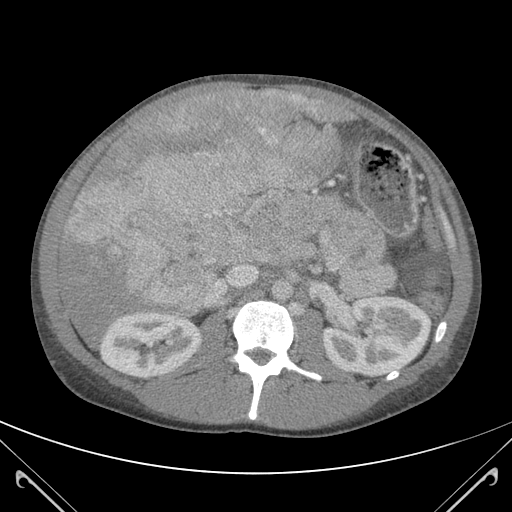
Contrast-enhanced abdominal CT (liver protocol), one axial slice; slice 61 of 118 in the series (ordered by position); 120 kVp; soft-tissue window (W 400 / L 40 HU); 512 × 512 image matrix, field of view 380 × 380 mm. From the clinical record (not read from this slice): diagnosis: hepatocellular carcinoma (patient treated with transarterial chemoembolisation; whether this scan precedes or follows treatment is not stated here); TNM stage (as recorded): Stage-IIIB; Child-Pugh class: A; tumour nodularity: uninodular.
Structures marked on this image (semi-automatic segmentation, software-assisted and operator-edited):
- abdominal aorta: bounding box <272,279,291,300> (left, top, right, bottom; pixels)
- liver parenchyma outside the tumour (the mass and vessels are separate outlines, so this box may not span the whole liver): <57,89,349,345>
- mass: <69,91,336,320>
- liver vessels: <206,246,259,303>